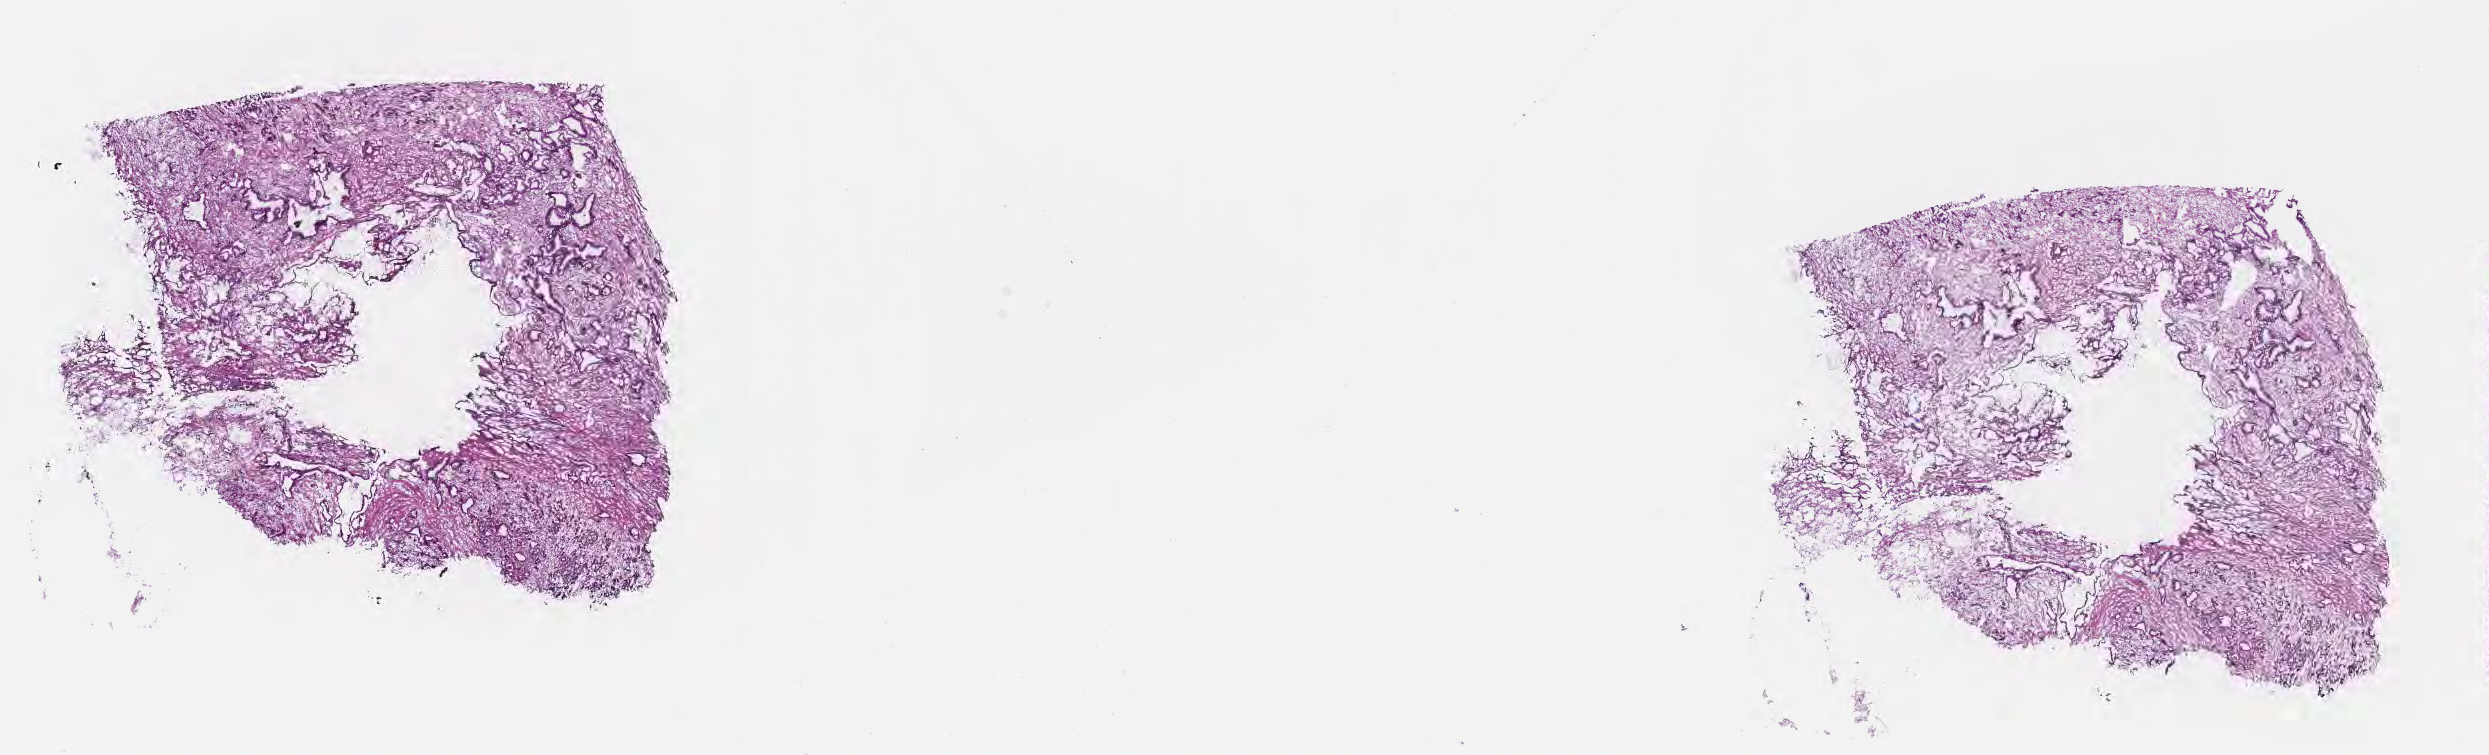
Whole-slide image, H&E stain — a low-resolution overview of the entire scanned area, about 20.1 x 6.1 mm. Cryosection. Specimen: primary tumor. Site: head of pancreas. Male patient; age at initial diagnosis 63 years. Tumor grade: G2 (moderately differentiated). Pathologist review of this section (percent, as recorded): tumor cells 20%, tumor nuclei 30%, stromal cells 40%, necrosis 0%, normal cells 40%. Infiltration values recorded for this section: lymphocyte infiltration 0%, monocyte infiltration 0%, neutrophil infiltration 0%.
• histologic diagnosis: Infiltrating duct carcinoma, NOS
• section: bottom of the tissue portion
• AJCC pathologic stage: Stage III